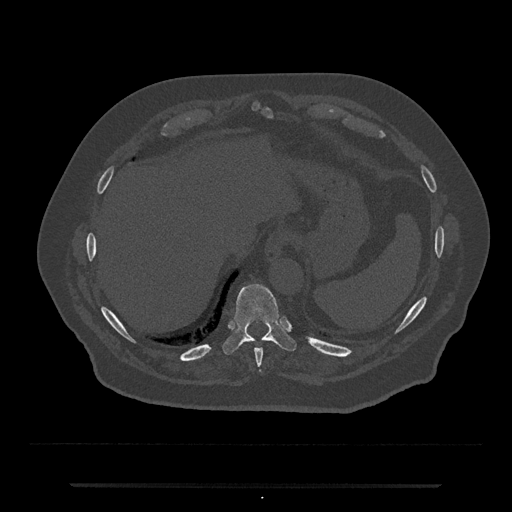
CT including the spine, one axial slice. Slice 720 of 797 in the series (ordered by position). Reconstruction kernel Br40s/3. Bone window (W 1800 / L 400 HU). 512 × 512 image matrix, field of view 434 × 434 mm. Patient: male, 80 years. From the clinical record (not read from this slice): primary cancer: prostate.
Outlined on this slice (semi-automatic segmentation, software-assisted and operator-edited):
- T10 vertebra: bounding box <222,284,297,355> (left, top, right, bottom; pixels)
- T9 vertebra: <254,348,263,373>